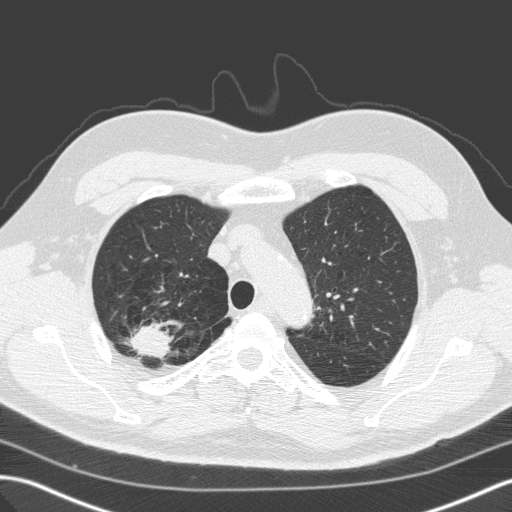
Low-dose screening chest CT, one axial slice. Position 121 of 149 along the scan axis. Lung window (W 1500 / L -600 HU). 512 × 512 image matrix.
Annotated regions visible in this slice (expert manual segmentation):
- lesion 1 (tumor, upper lobe of right lung): bounding box [x1, y1, x2, y2] px = [128, 324, 173, 357]